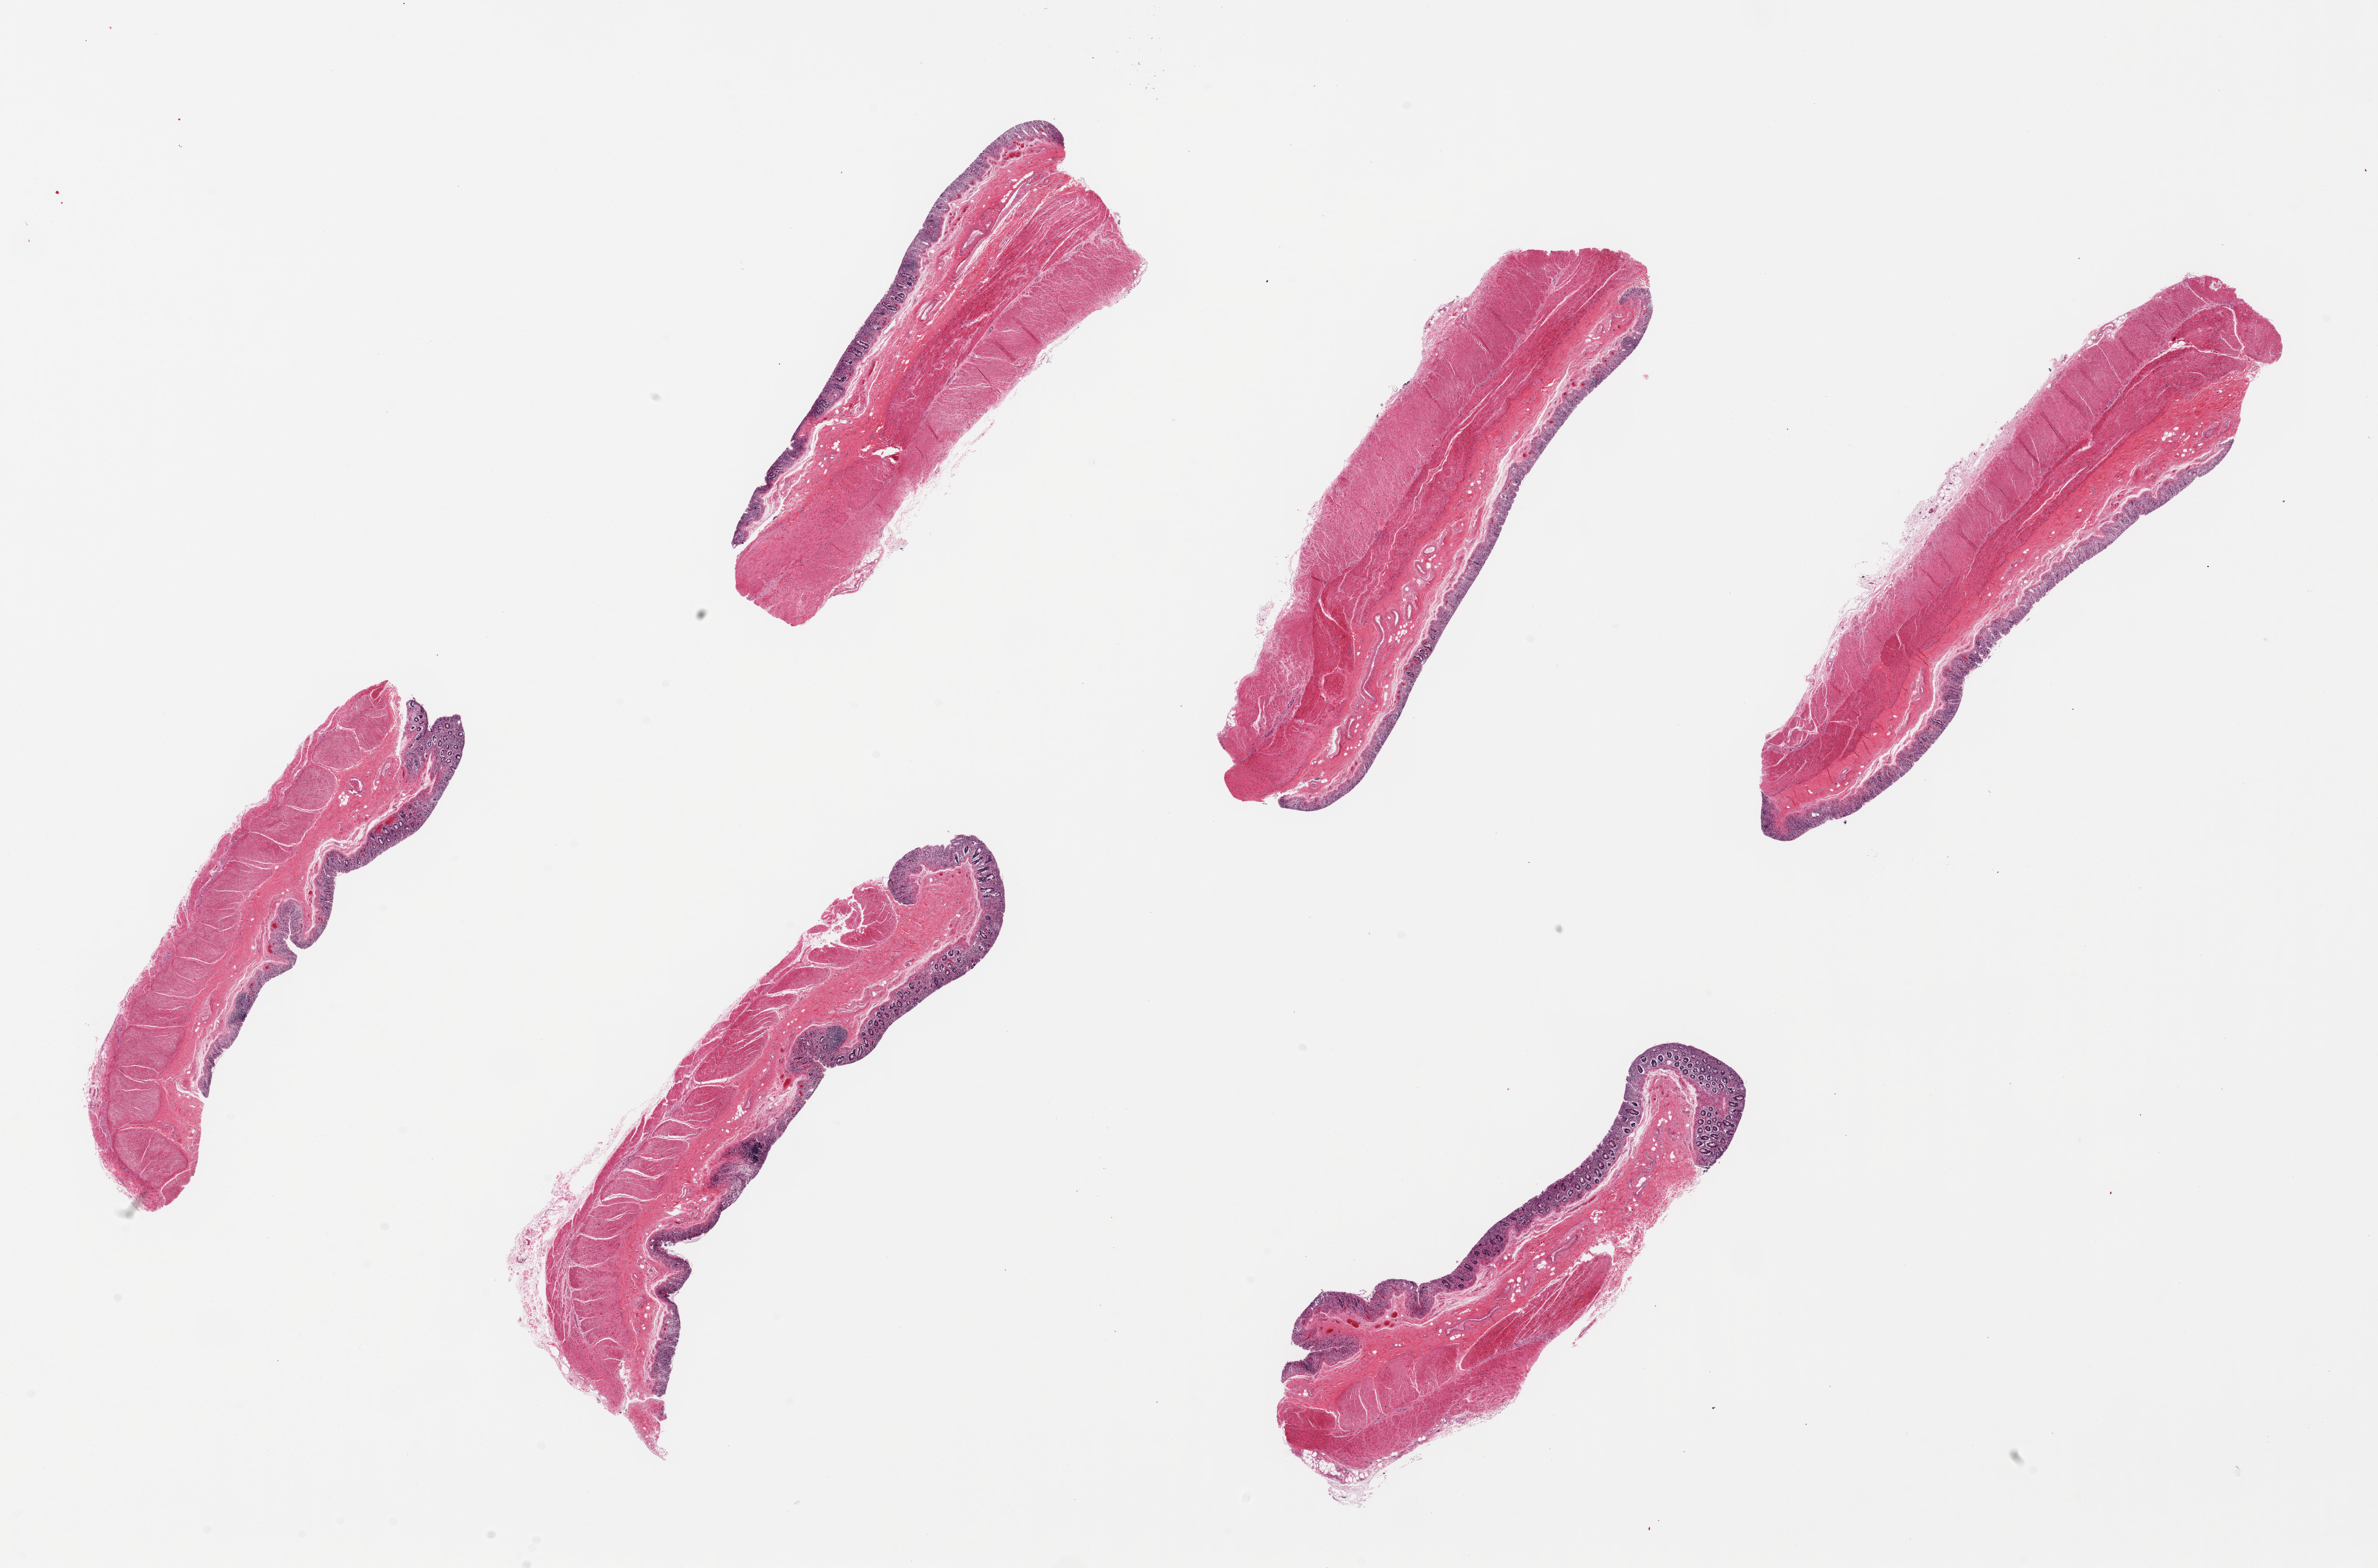
Whole-slide image, hematoxylin and eosin (H&E) stain, brightfield — shown as a low-resolution overview of the whole scanned area (about 31.5 x 20.8 mm). PAXgene-fixed, paraffin-embedded tissue. Target tissue: transverse colon. Donor tissue sample. Female donor.
Reviewer comment on this tissue sample: 6 pieces, up to 9.5x2mm; autolysis ranges from moderate to severe.